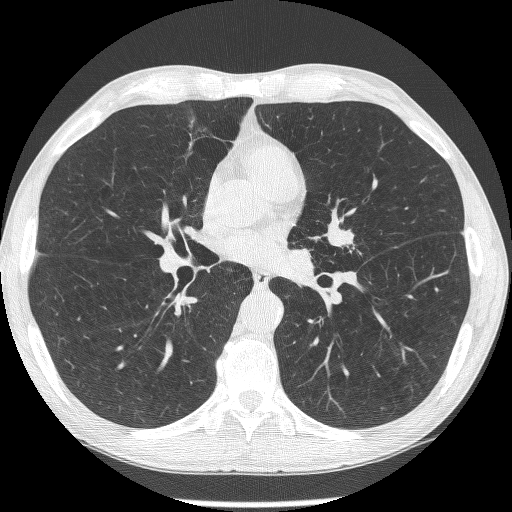
Low-dose screening chest CT, axial slice; second annual screen; lung window (W 1500 / L -600 HU); 1.25 mm slice thickness; 120 kVp; slice 139 of 293 in the series. Male, age 62 years at enrolment. Former smoker at enrolment.
- Expert reader's lesion annotation, box from (x=319, y=217) to (x=368, y=265) px.
- The screening reader recorded 2 non-calcified nodules or masses ≥4 mm on this exam (lingula, lingula); which of them this box marks is not recorded.
- Later outcome: lung cancer diagnosed 95 days after this screen — small cell carcinoma, NOS, left upper lobe, stage IIIA (AJCC 6th edition).